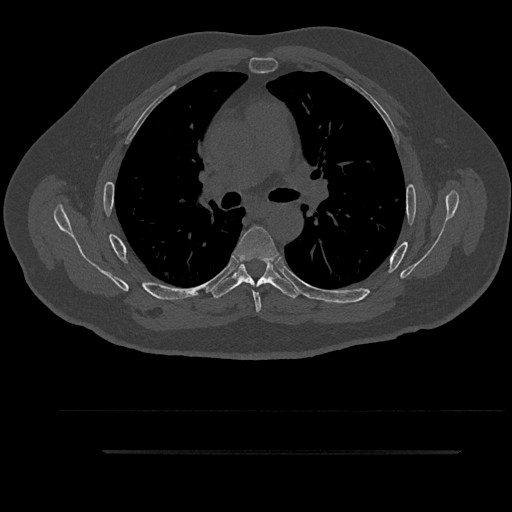
CT including the spine, one axial slice; position 603 of 797 along the scan axis; 120 kVp; bone window (W 1800 / L 400 HU); 0.5 mm slice thickness; 512 × 512 image matrix, field of view 432 × 432 mm. Male patient, age 63 years. Case-level facts recorded for this patient, not image findings: primary cancer: renal.
Annotated regions visible in this slice (semi-automatic segmentation, software-assisted and operator-edited):
- T5 vertebra: box from (x=233, y=226) to (x=280, y=312) px
- T6 vertebra: (x=211, y=257)–(x=300, y=298)